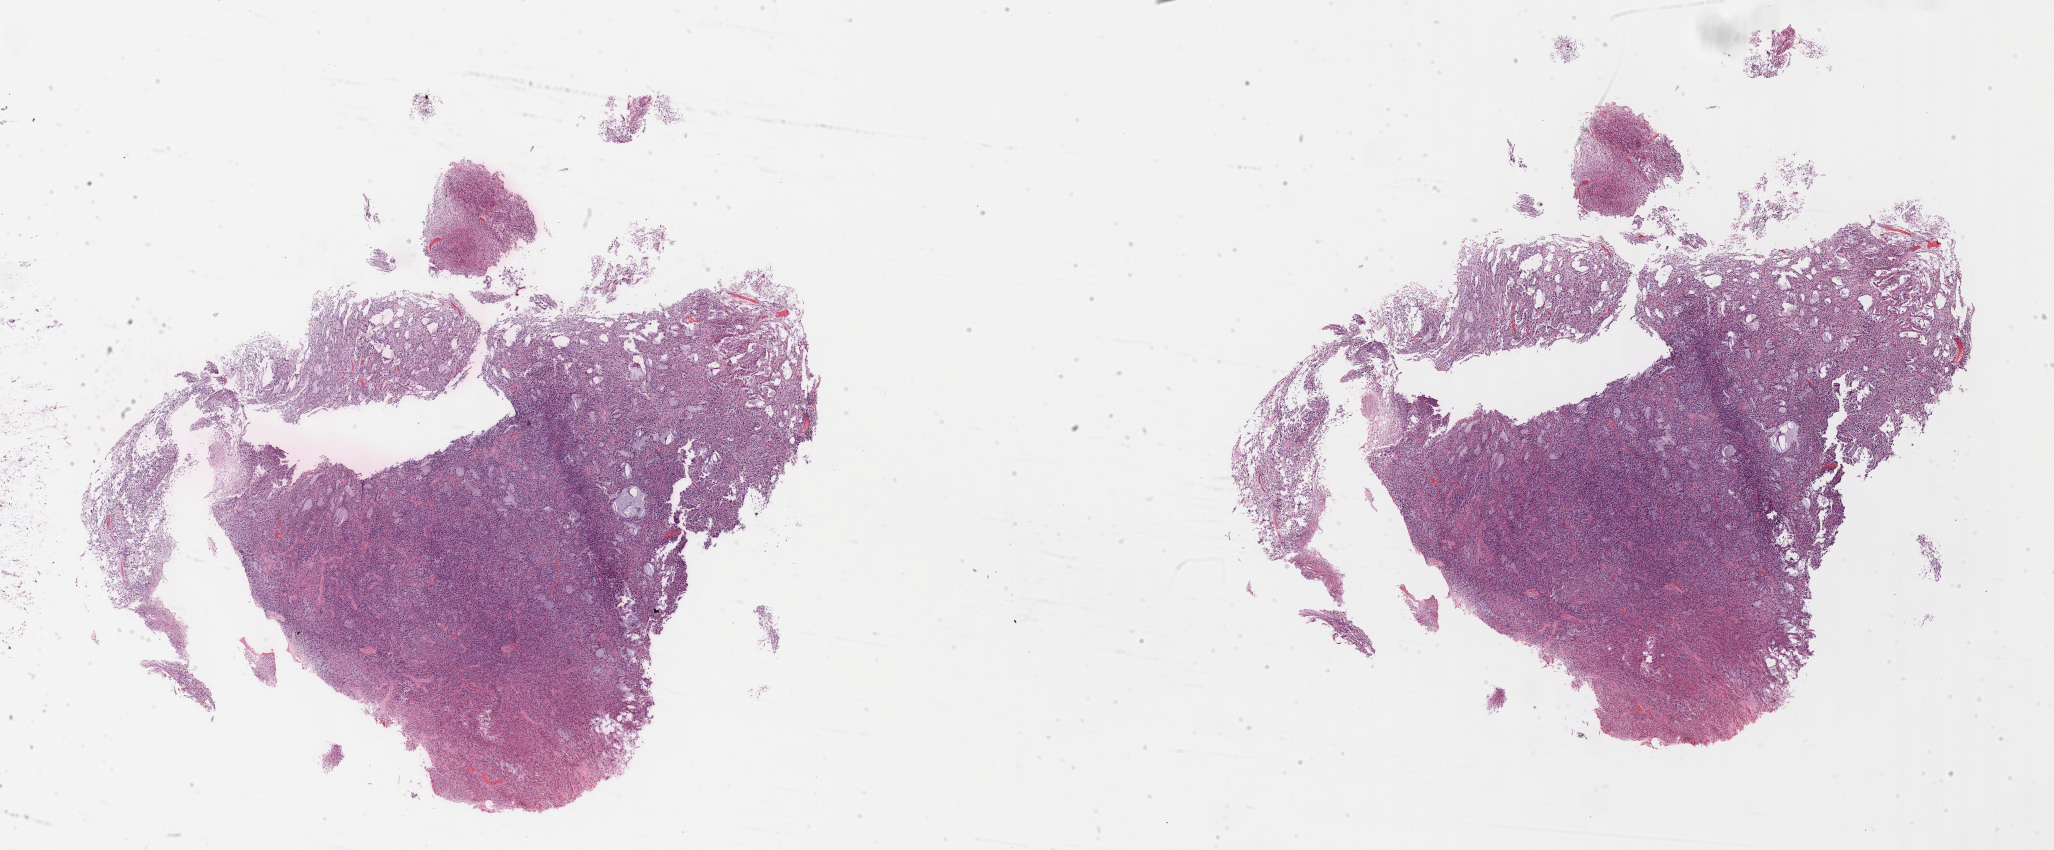
Whole-slide histology image, Hematoxylin and eosin (H&E) stained — a low-resolution overview of the entire scanned area, about 33.2 x 13.7 mm, formalin-fixed paraffin-embedded (FFPE) diagnostic section, primary tumour sample from the brain. Female patient; age at initial diagnosis 36 years.
Histologic diagnosis: Astrocytoma, anaplastic (cerebrum).